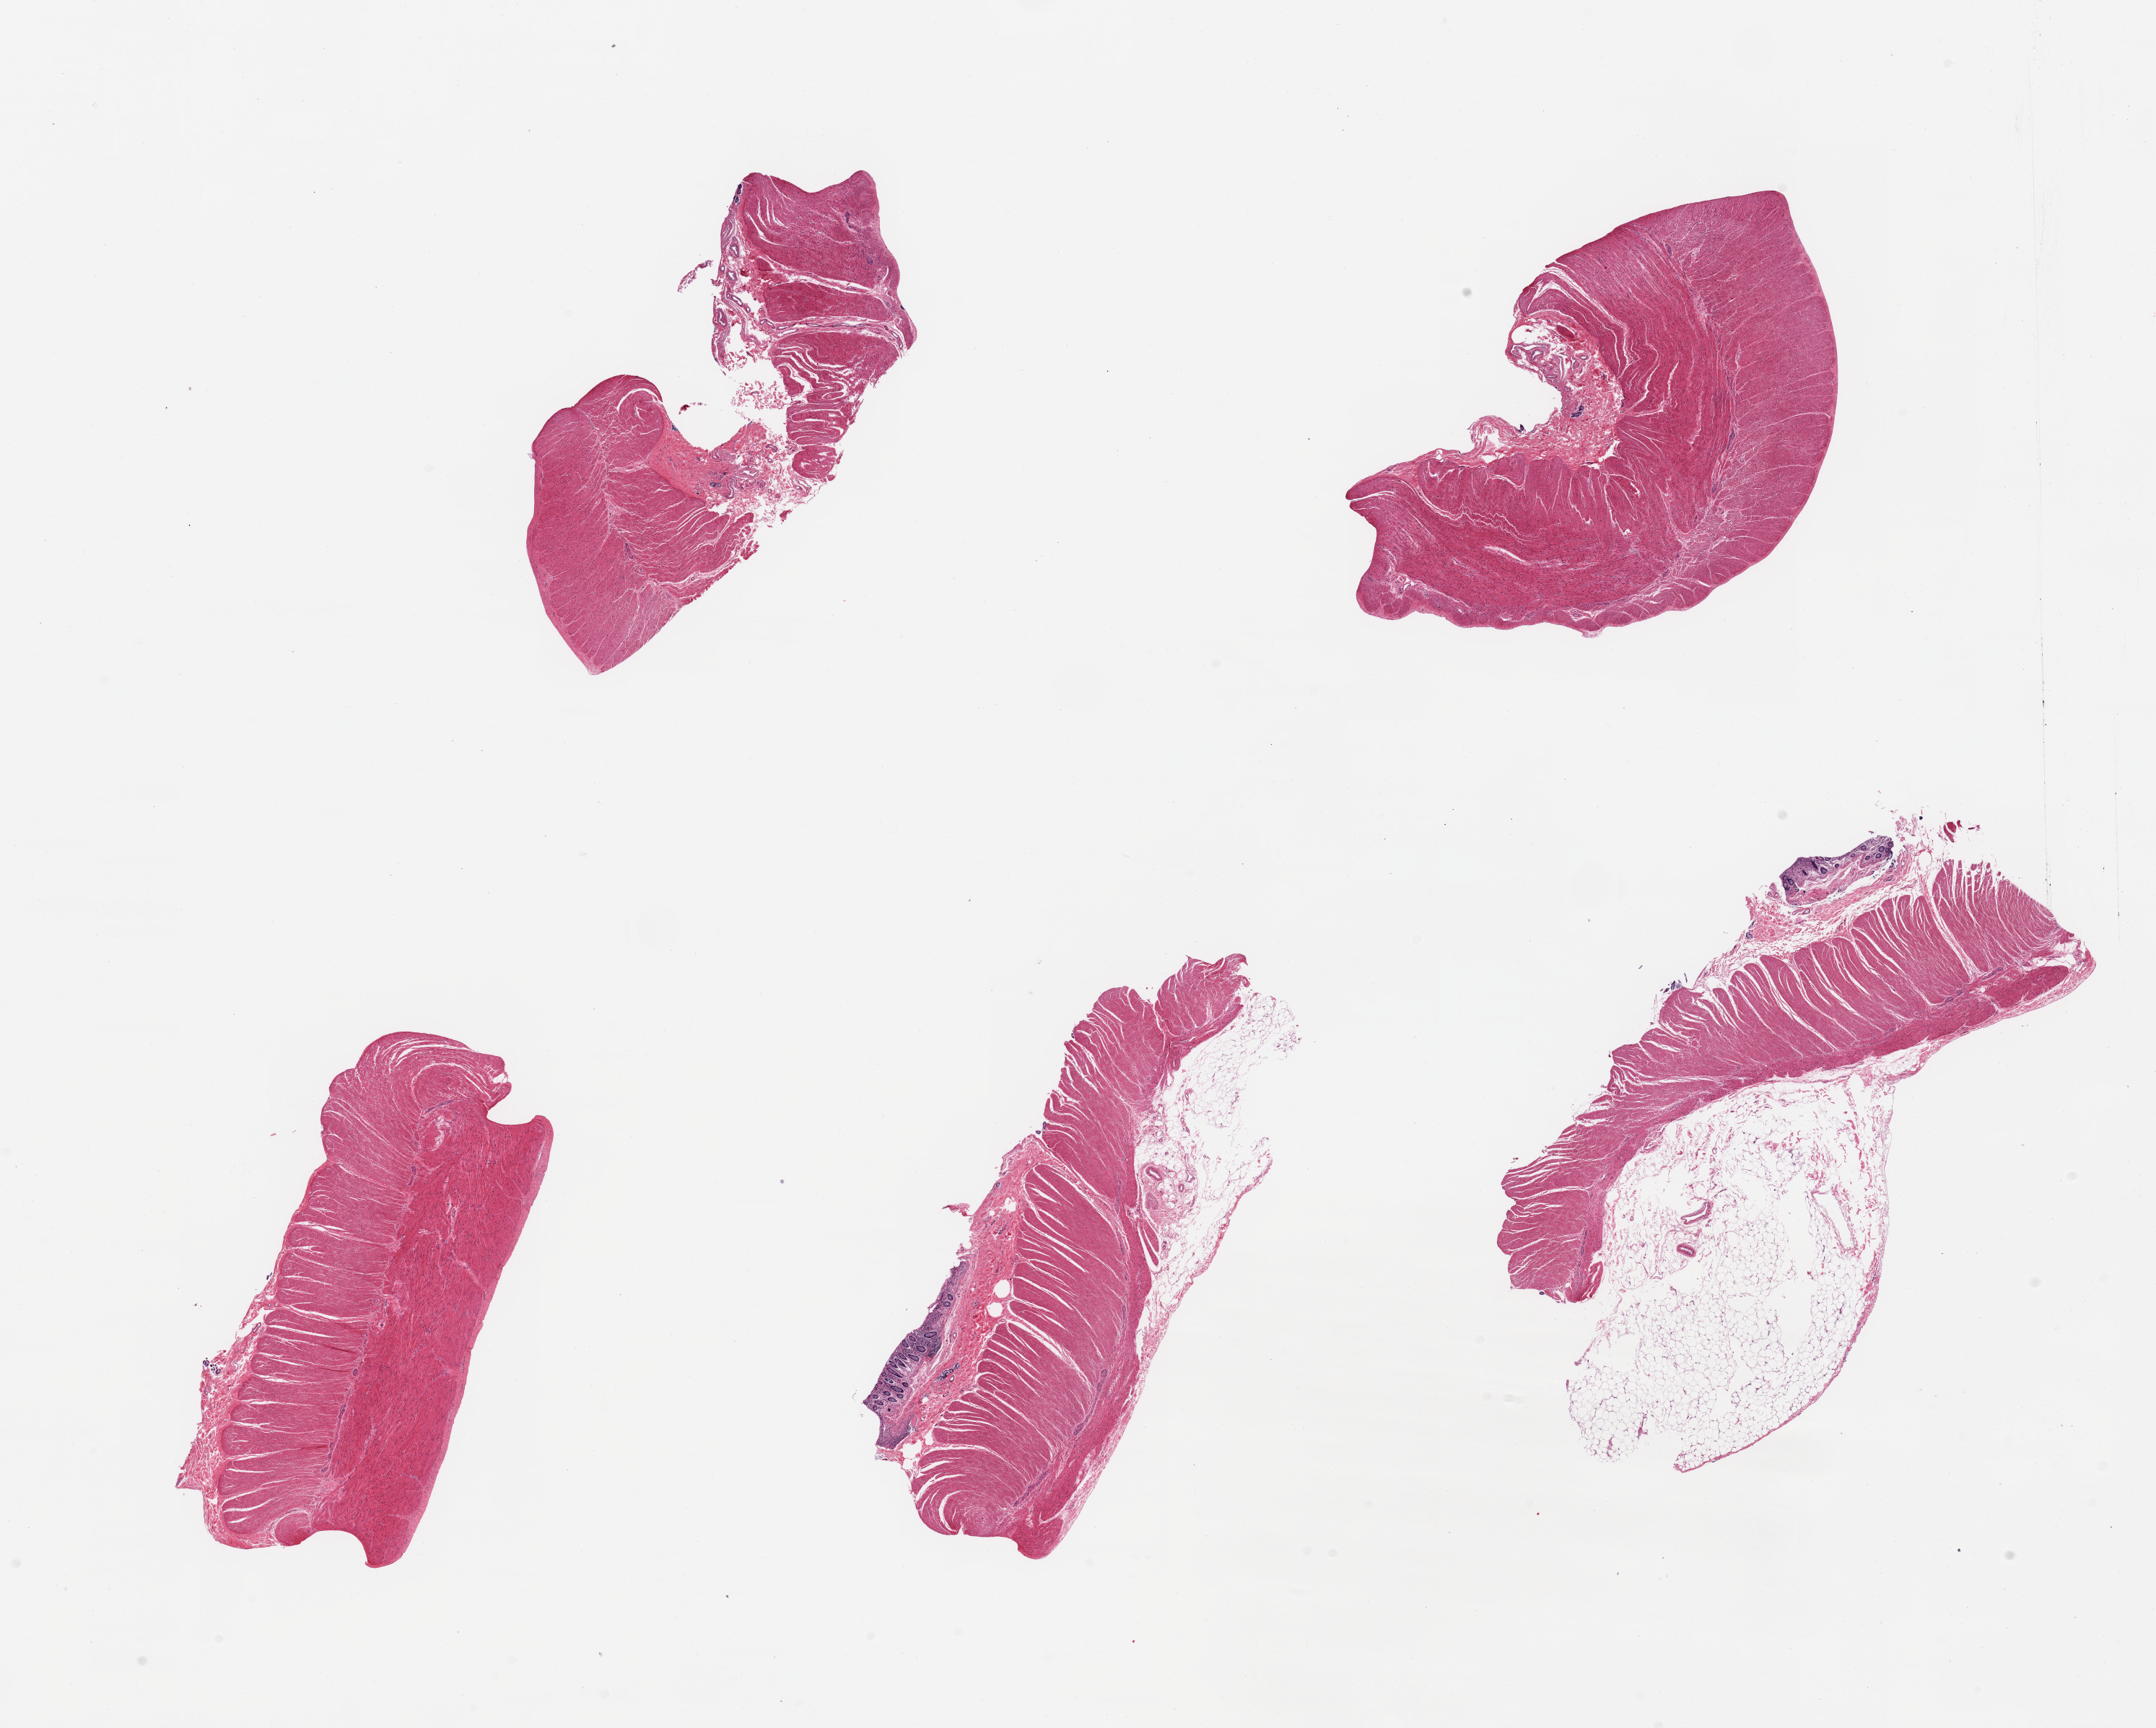
Whole-slide image, H&E stain, brightfield, a low-resolution overview of the entire scanned area, about 23.6 x 18.9 mm; PAXgene-fixed paraffin-embedded (PFPE) section; sampled site (target tissue): sigmoid colon; tissue donor sample. Donor sex: female.
Review note (as recorded): 5 pieces; two pieces with small fragments of mucosa and serosal fat.